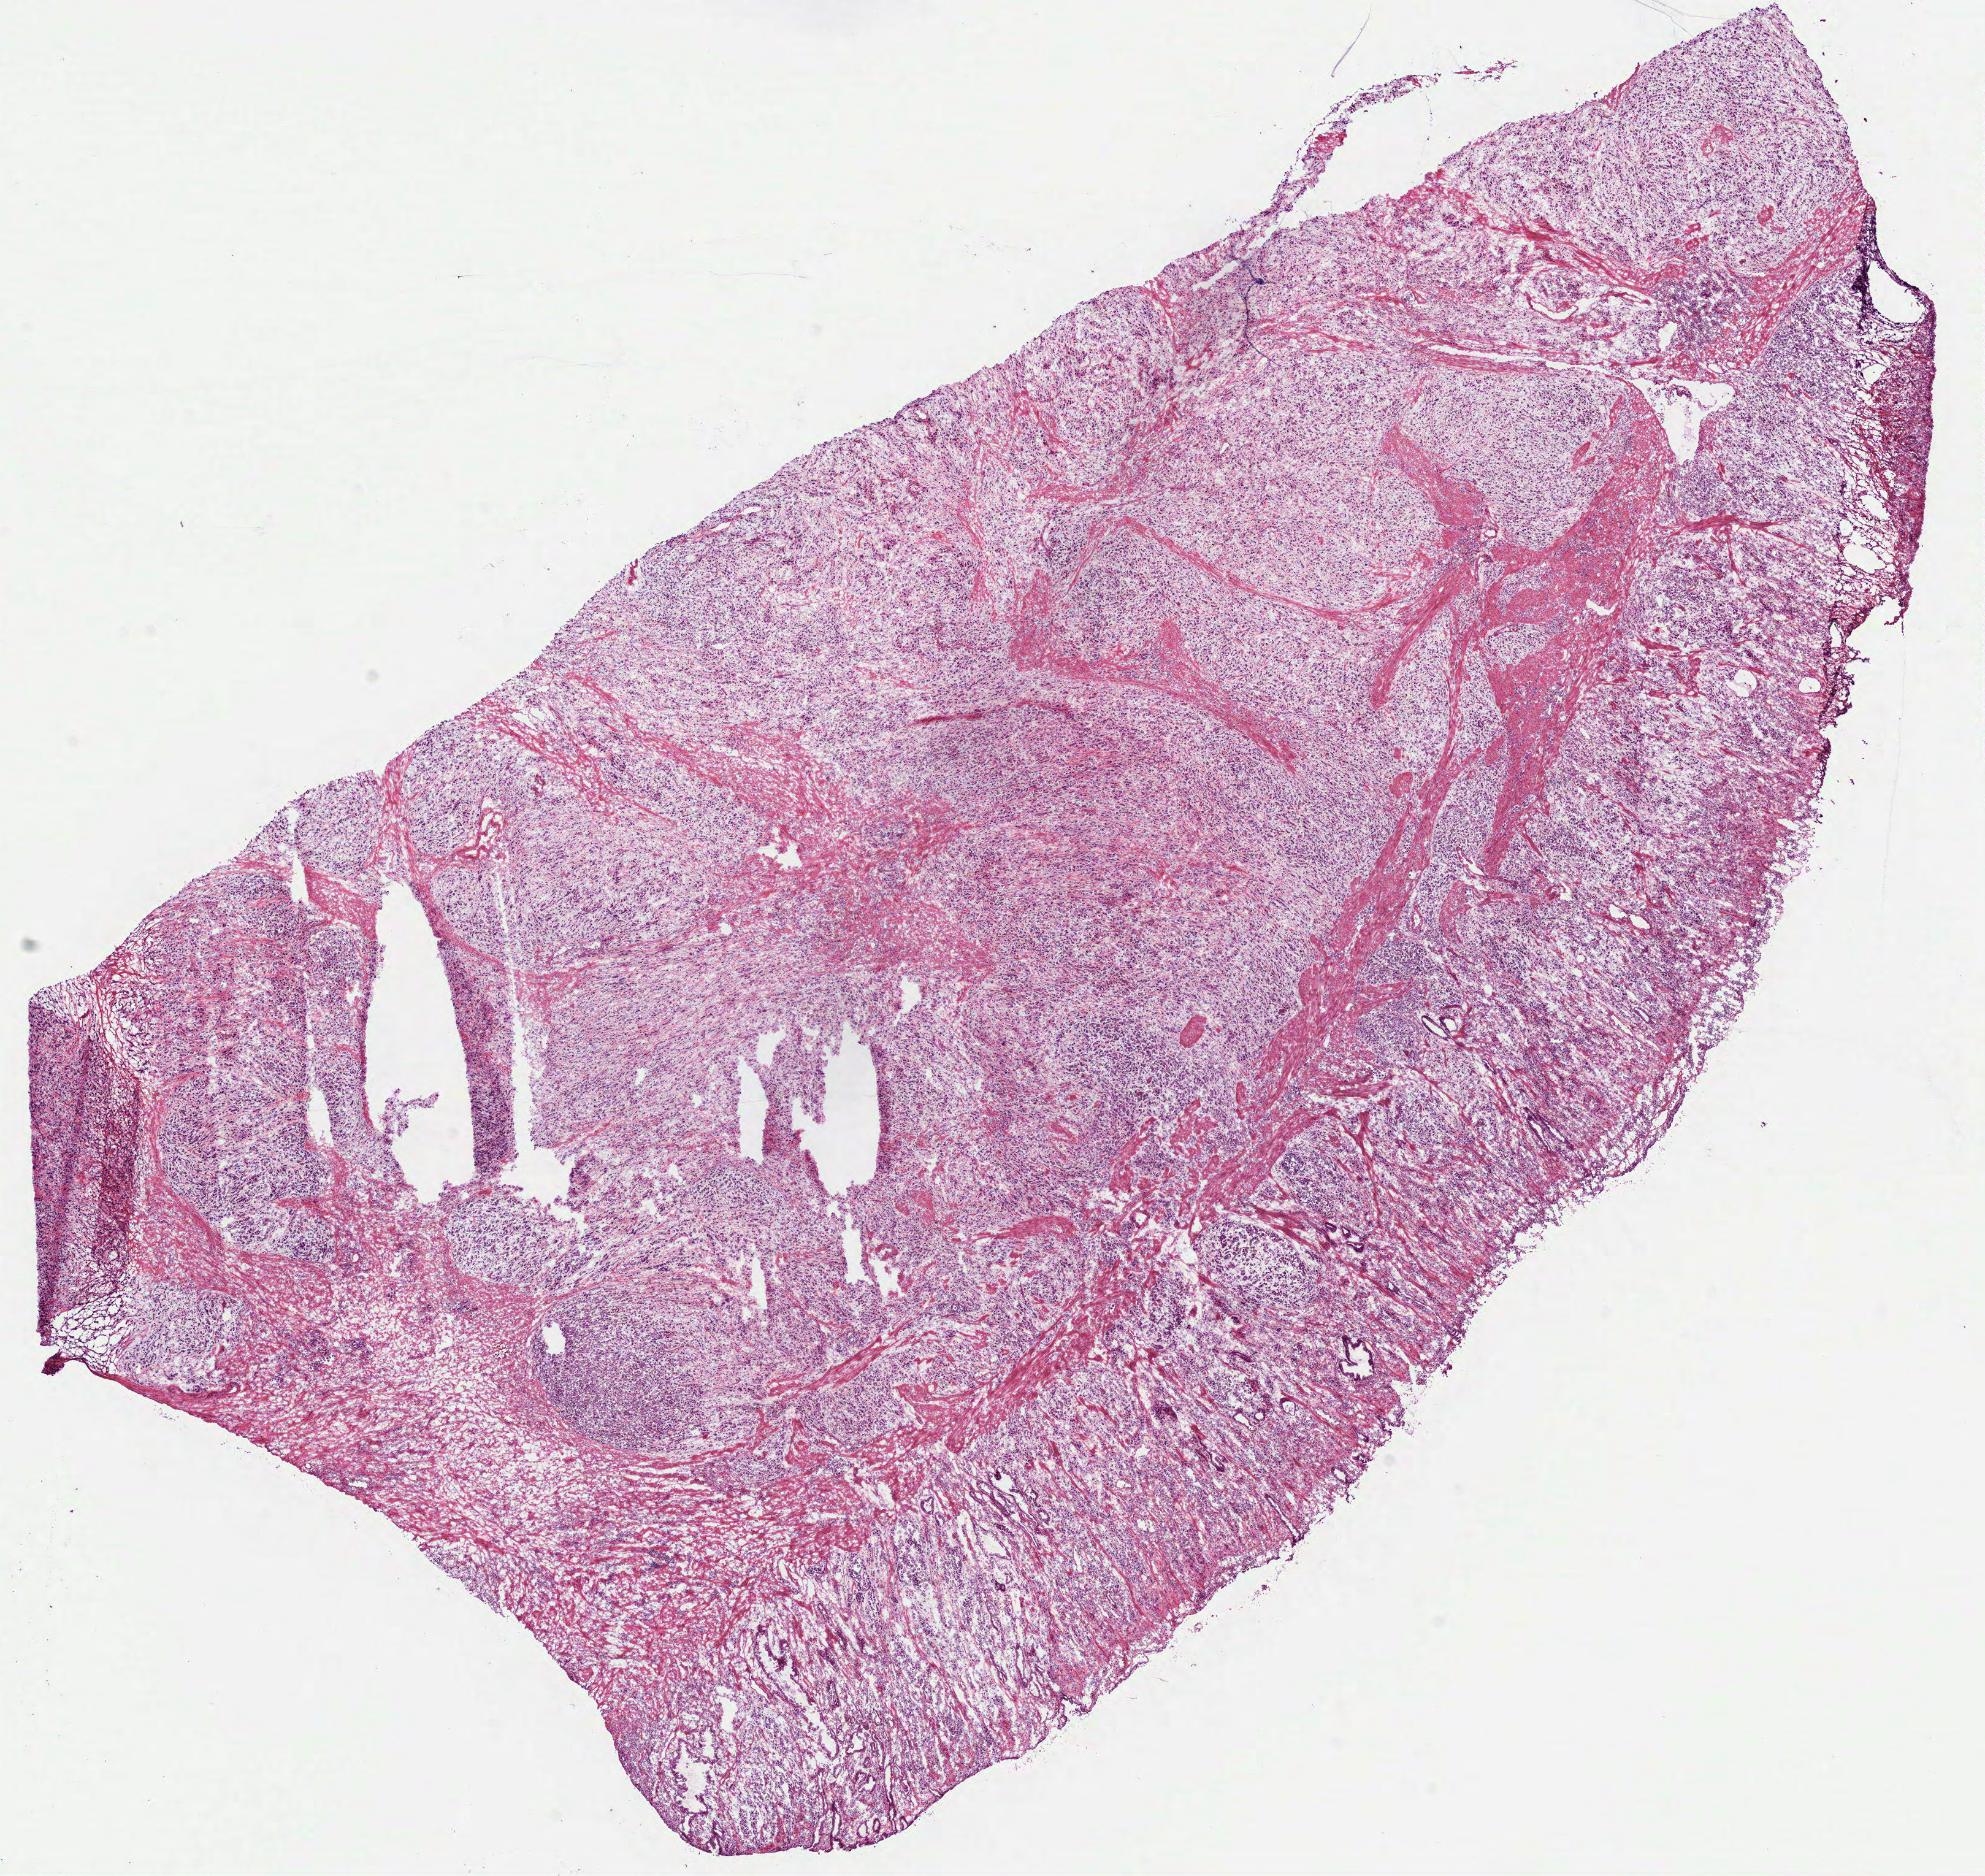
Whole-slide histology image, H&E-stained, whole scanned area (about 13.1 x 12.3 mm, from a 40x scan) shown as a low-resolution overview; frozen section from the bottom of the tissue portion; stomach, primary tumour sample. Male patient; age at initial diagnosis 51 years.
Pathologic diagnosis: Carcinoma, diffuse type (fundus of stomach).